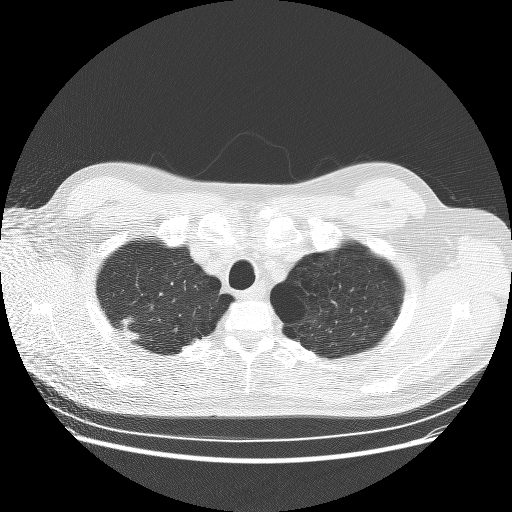
Low-dose screening chest CT, one axial slice. Slice 230 of 253 in the series (ordered by position). Reconstruction kernel BONE. Lung window (W 1500 / L -600 HU). 2.5 mm slice thickness. 512 × 512 image matrix, field of view 370 × 370 mm.
Outlined on this slice (outlined manually by an expert reader):
- lesion 1 (tumor, upper lobe of right lung): box from (x=122, y=318) to (x=140, y=340) px